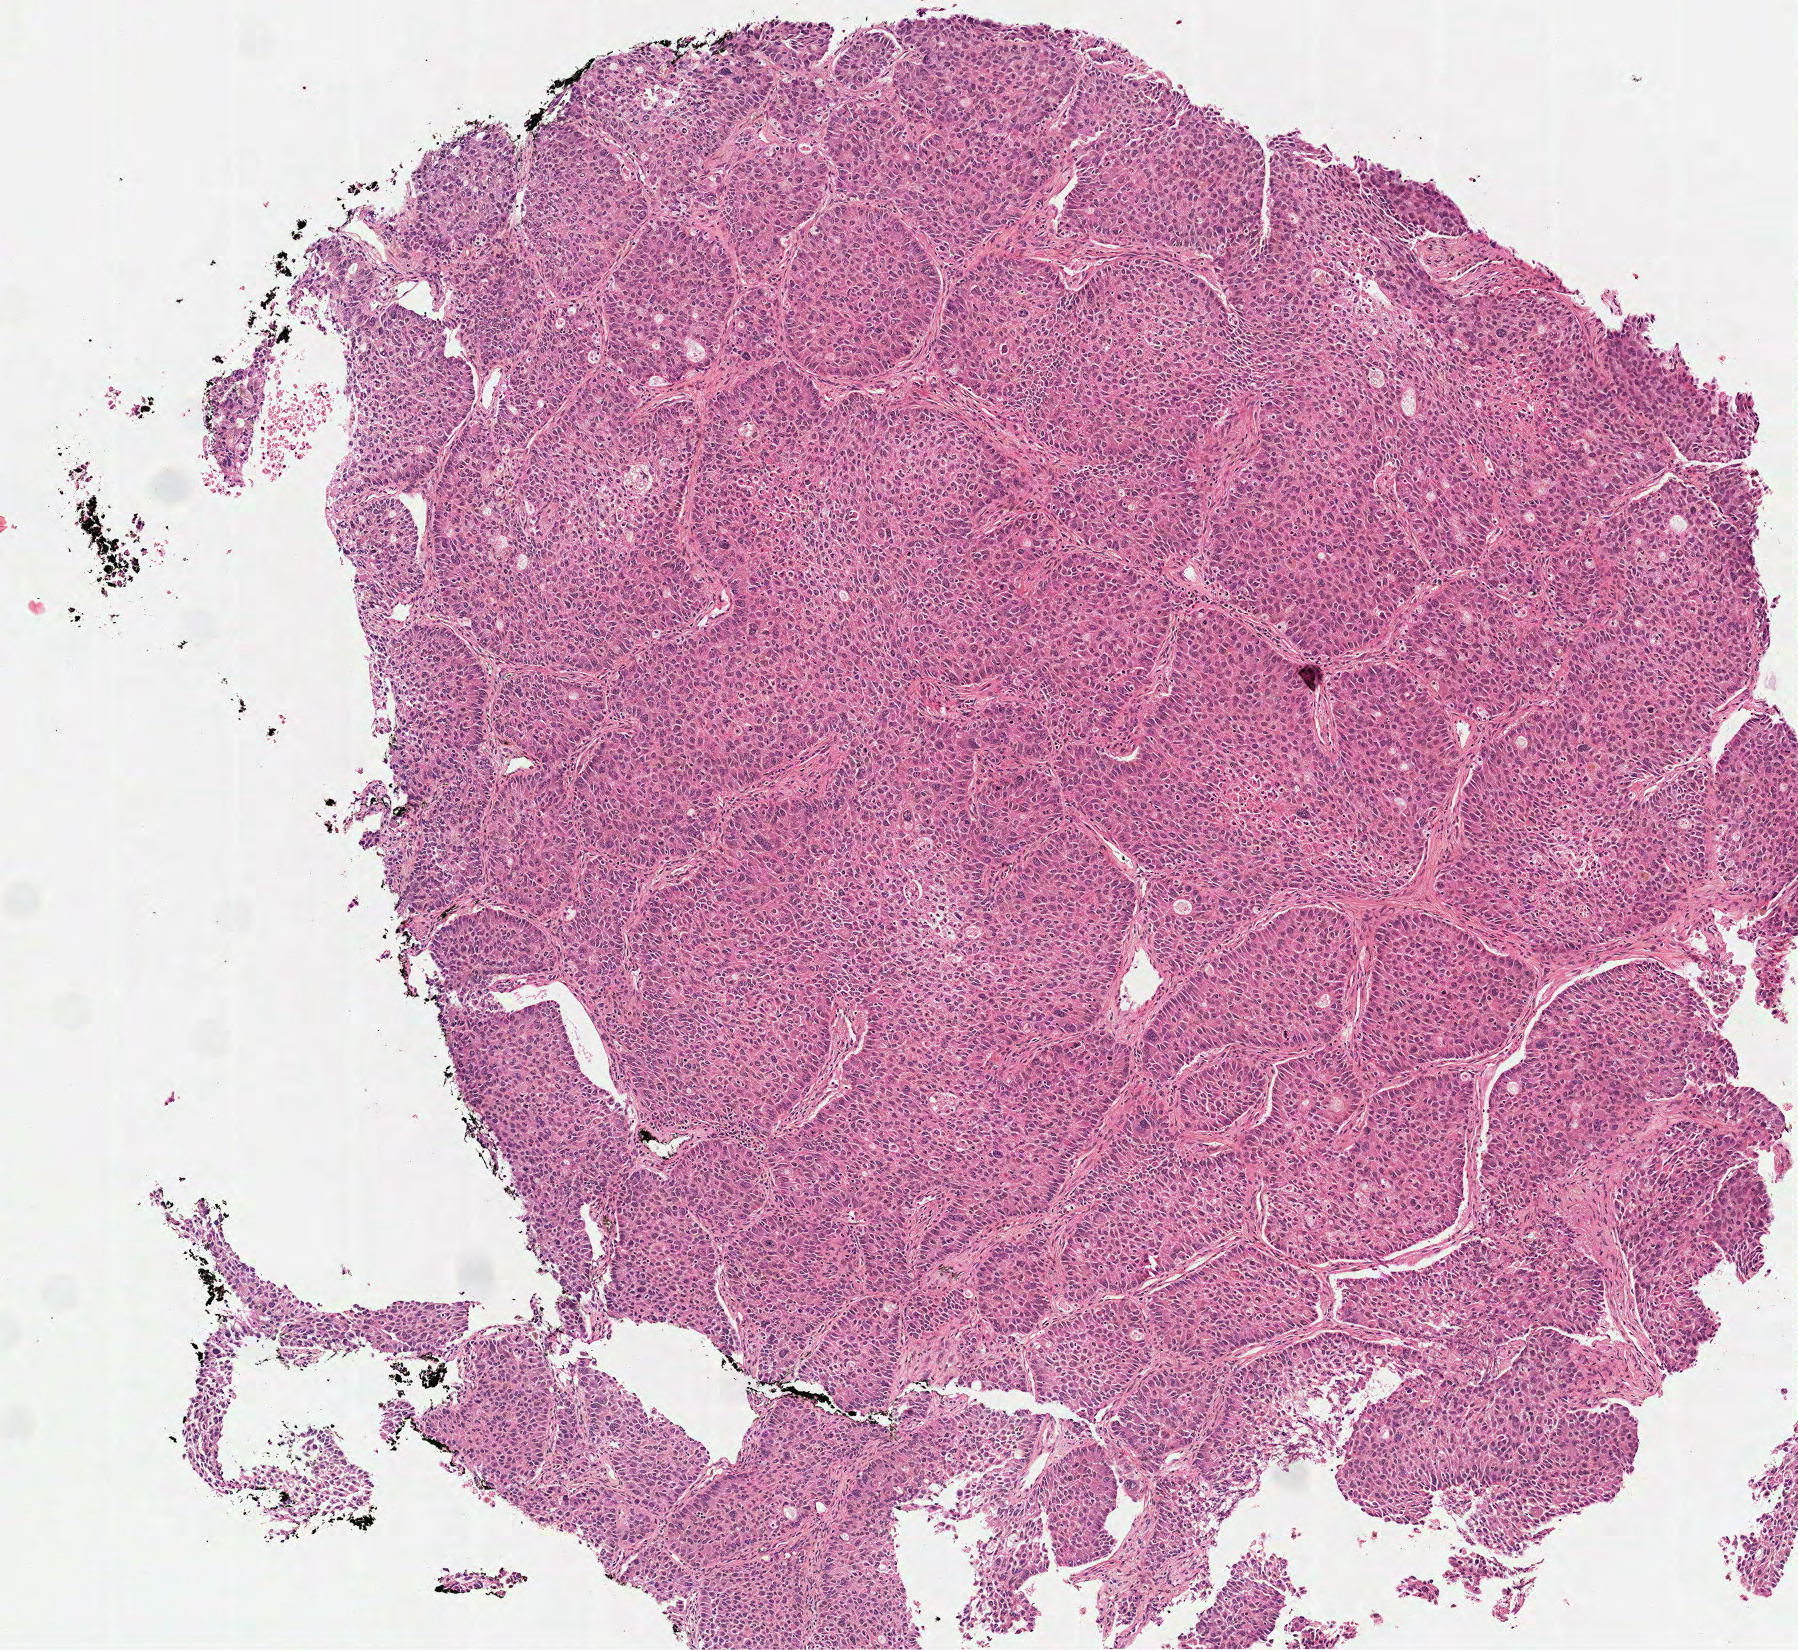
Digitized H&E-stained tissue section (whole slide), whole scanned area (about 3.6 x 3.3 mm, slide scanned at 40x) shown as a low-resolution overview. Frozen section from the top of the tissue portion. Sample: primary tumour, lung. Patient: female, age at initial diagnosis 53 years.
Diagnosis: Adenocarcinoma with mixed subtypes.